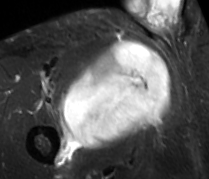
MRI of an extremity soft-tissue mass, one axial slice. Slice 56 of 89 in the series (ordered by position). STIR. MR volume resampled by the dataset authors to the PET/CT grid (not the native acquisition matrix). 3.27 mm slice thickness. 209 × 179 image matrix, field of view 204 × 175 mm. Male patient. From the clinical record (not read from this slice): histological type: undifferentiated - pleiomorphic; grade: high; site of the primary tumour: right thigh.
Outlined on this slice (expert contour drawn on MRI and transferred to this co-registered scan by the dataset authors):
- gross tumour volume including surrounding oedema: bounding box [x1, y1, x2, y2] px = [59, 41, 170, 149]
- gross tumour volume (mass): [60, 41, 170, 149]